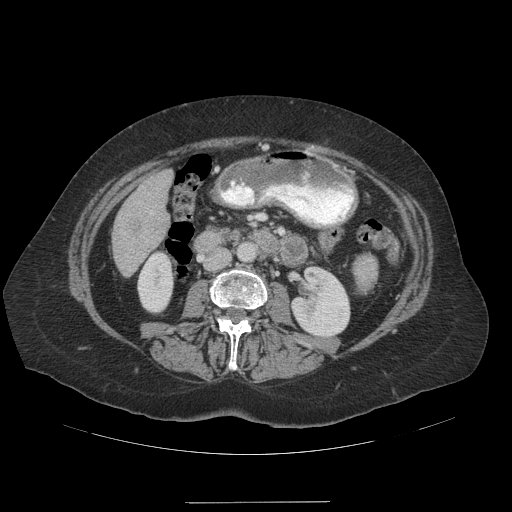
Contrast-enhanced abdominal CT (liver protocol), one axial slice. Slice 39 of 99 in the series (ordered by position). 140 kVp. Soft-tissue window (W 400 / L 40 HU). 2.5 mm slice thickness. 512 × 512 image matrix. From the clinical record (not read from this slice): diagnosis: hepatocellular carcinoma (patient treated with transarterial chemoembolisation; whether this scan precedes or follows treatment is not stated here); TNM stage (as recorded): Stage-IVA; Child-Pugh class: A; tumour nodularity: multinodular.
Outlined on this slice (semi-automatically segmented with operator editing):
- liver parenchyma outside the tumour (the mass and vessels are separate outlines, so this box may not span the whole liver): bounding box (x1, y1, x2, y2) in pixels: (112, 170, 172, 276)